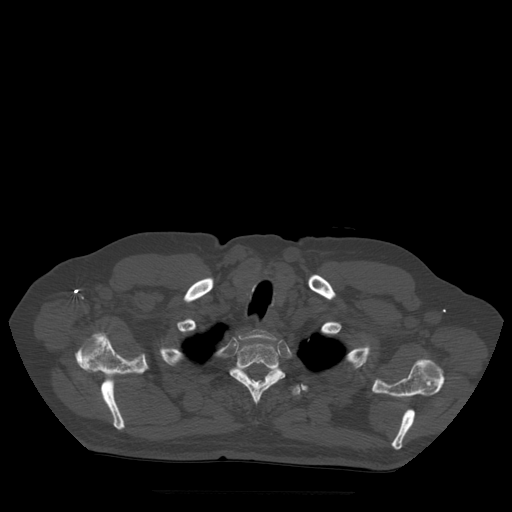
CT including the spine, one axial slice. Slice 424 of 522 in the series (ordered by position). Bone window (W 1800 / L 400 HU). 1.25 mm slice thickness. 512 × 512 image matrix, field of view 420 × 420 mm. Patient age 72 years. Case-level facts recorded for this patient, not image findings: primary cancer: prostate.
Annotated regions visible in this slice (semi-automatic segmentation, software-assisted and operator-edited):
- T1 vertebra: box from (x=239, y=330) to (x=277, y=340) px
- T2 vertebra: (x=230, y=337)–(x=286, y=403)
- T3 vertebra: (x=239, y=367)–(x=301, y=396)